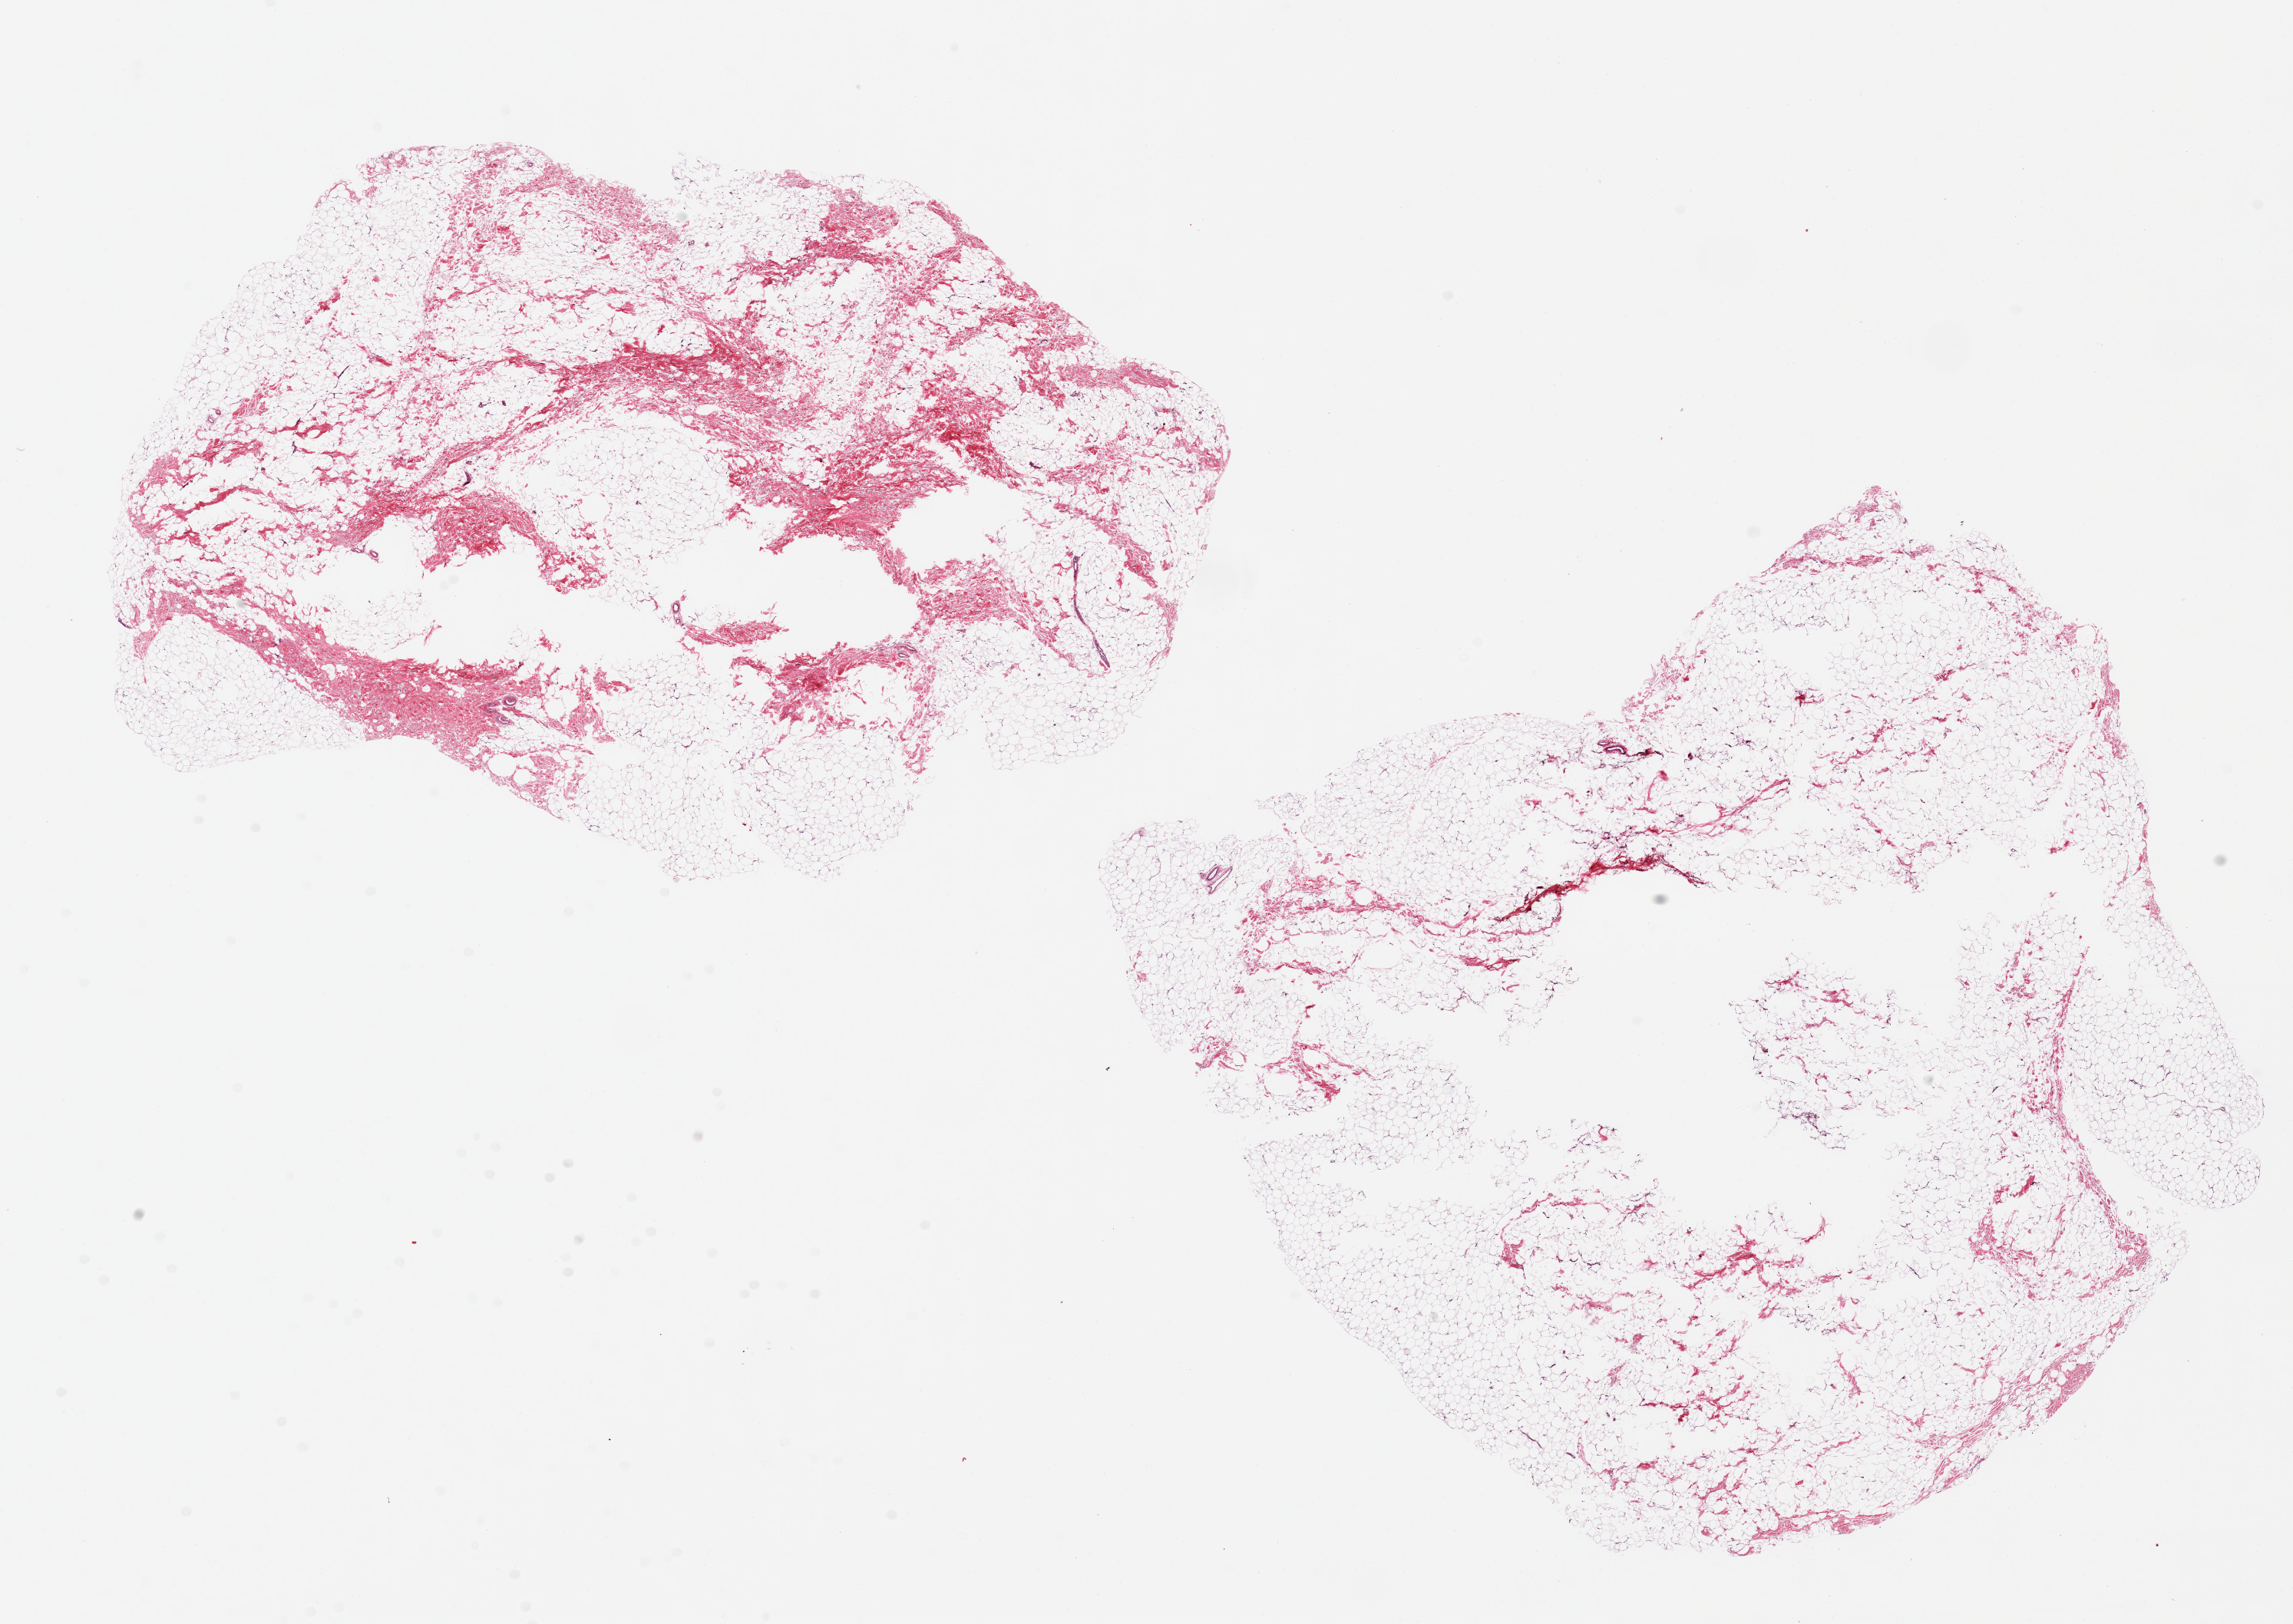
Haematoxylin and eosin whole-slide image — whole scanned area (about 23.6 x 16.7 mm, from a 20x scan) shown as a low-resolution overview. PAXgene-fixed, paraffin-embedded tissue. Section of breast (target tissue). Tissue donor sample. Donor: male.
Review note (as recorded): 2 pieces 11x10mm. All fibroadipose.